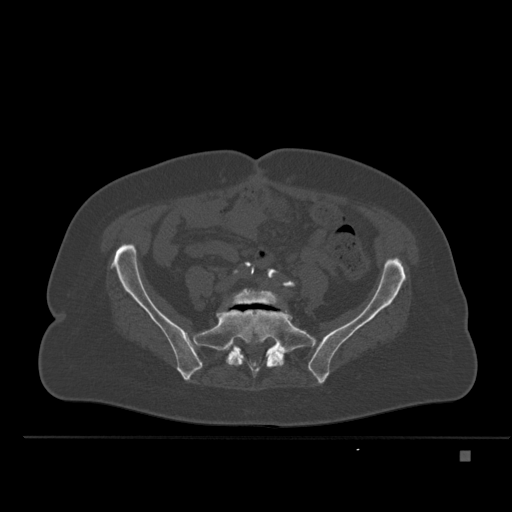
CT including the spine, one axial slice; slice 148 of 477 in the series (ordered by position); bone window (W 1800 / L 400 HU); 1.5 mm slice thickness; 512 × 512 image matrix. Patient: female, 74 years. From the clinical record (not read from this slice): primary cancer: colon.
Structures marked on this image (semi-automatic segmentation, software-assisted and operator-edited):
- L5 vertebra: bounding box <230,290,280,306> (left, top, right, bottom; pixels)